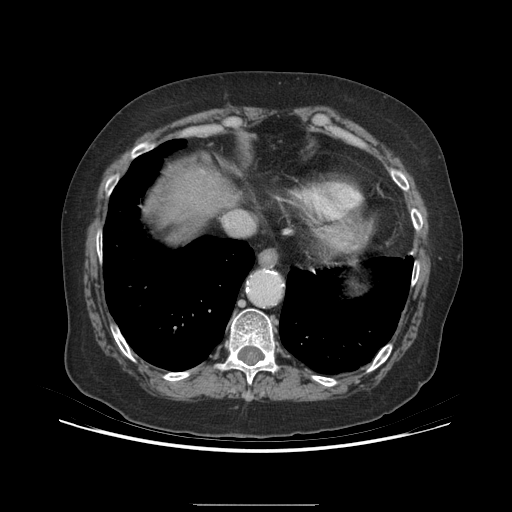
Contrast-enhanced abdominal CT (liver protocol), one axial slice; slice 180 of 192 in the series (ordered by position); 140 kVp; soft-tissue window (W 400 / L 40 HU); 512 × 512 image matrix, field of view 400 × 400 mm. Case-level facts recorded for this patient, not image findings: diagnosis: hepatocellular carcinoma (patient treated with transarterial chemoembolisation; whether this scan precedes or follows treatment is not stated here); TNM stage (as recorded): Stage-I; Child-Pugh class: A; tumour differentiation: moderately differentiated.
Annotated regions visible in this slice (semi-automatic segmentation, software-assisted and operator-edited):
- abdominal aorta: bounding box (x1, y1, x2, y2) in pixels: (250, 272, 280, 304)
- liver parenchyma outside the tumour (the mass and vessels are separate outlines, so this box may not span the whole liver): (148, 165, 232, 228)